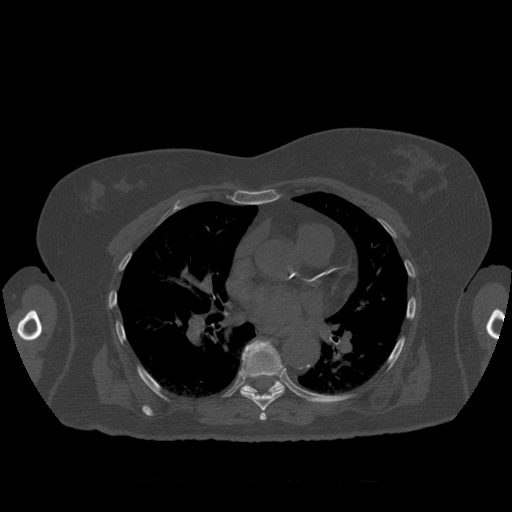
CT including the spine, one axial slice. Reconstruction kernel STANDARD. Bone window (W 1800 / L 400 HU). 512 × 512 image matrix. Patient age 81 years. Case-level facts recorded for this patient, not image findings: primary cancer: renal.
Outlined on this slice (semi-automatic segmentation, software-assisted and operator-edited):
- T7 vertebra: bounding box (x1, y1, x2, y2) in pixels: (240, 340, 284, 421)
- T8 vertebra: (241, 380, 285, 394)